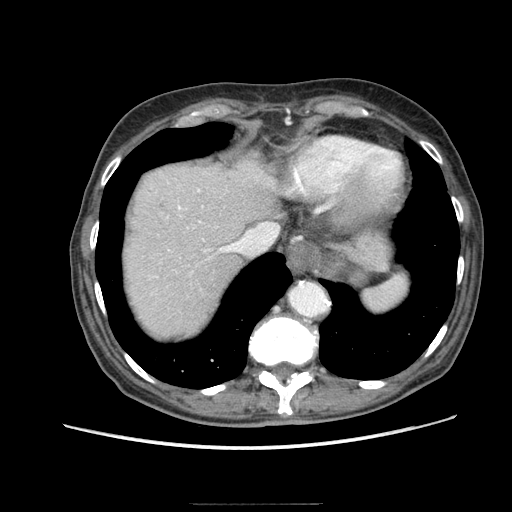
Contrast-enhanced abdominal CT (liver protocol), one axial slice; position 71 of 83 along the scan axis; reconstruction kernel STANDARD; 140 kVp; soft-tissue window (W 400 / L 40 HU); 2.5 mm slice thickness; 512 × 512 image matrix. From the clinical record (not read from this slice): diagnosis: hepatocellular carcinoma (patient treated with transarterial chemoembolisation; whether this scan precedes or follows treatment is not stated here); TNM stage (as recorded): Stage-I; Child-Pugh class: A; tumour nodularity: uninodular.
Structures marked on this image (semi-automatically segmented with operator editing):
- abdominal aorta: bounding box [x1, y1, x2, y2] px = [289, 283, 328, 316]
- liver parenchyma outside the tumour (the mass and vessels are separate outlines, so this box may not span the whole liver): [126, 158, 276, 336]
- liver vessels: [178, 190, 233, 252]